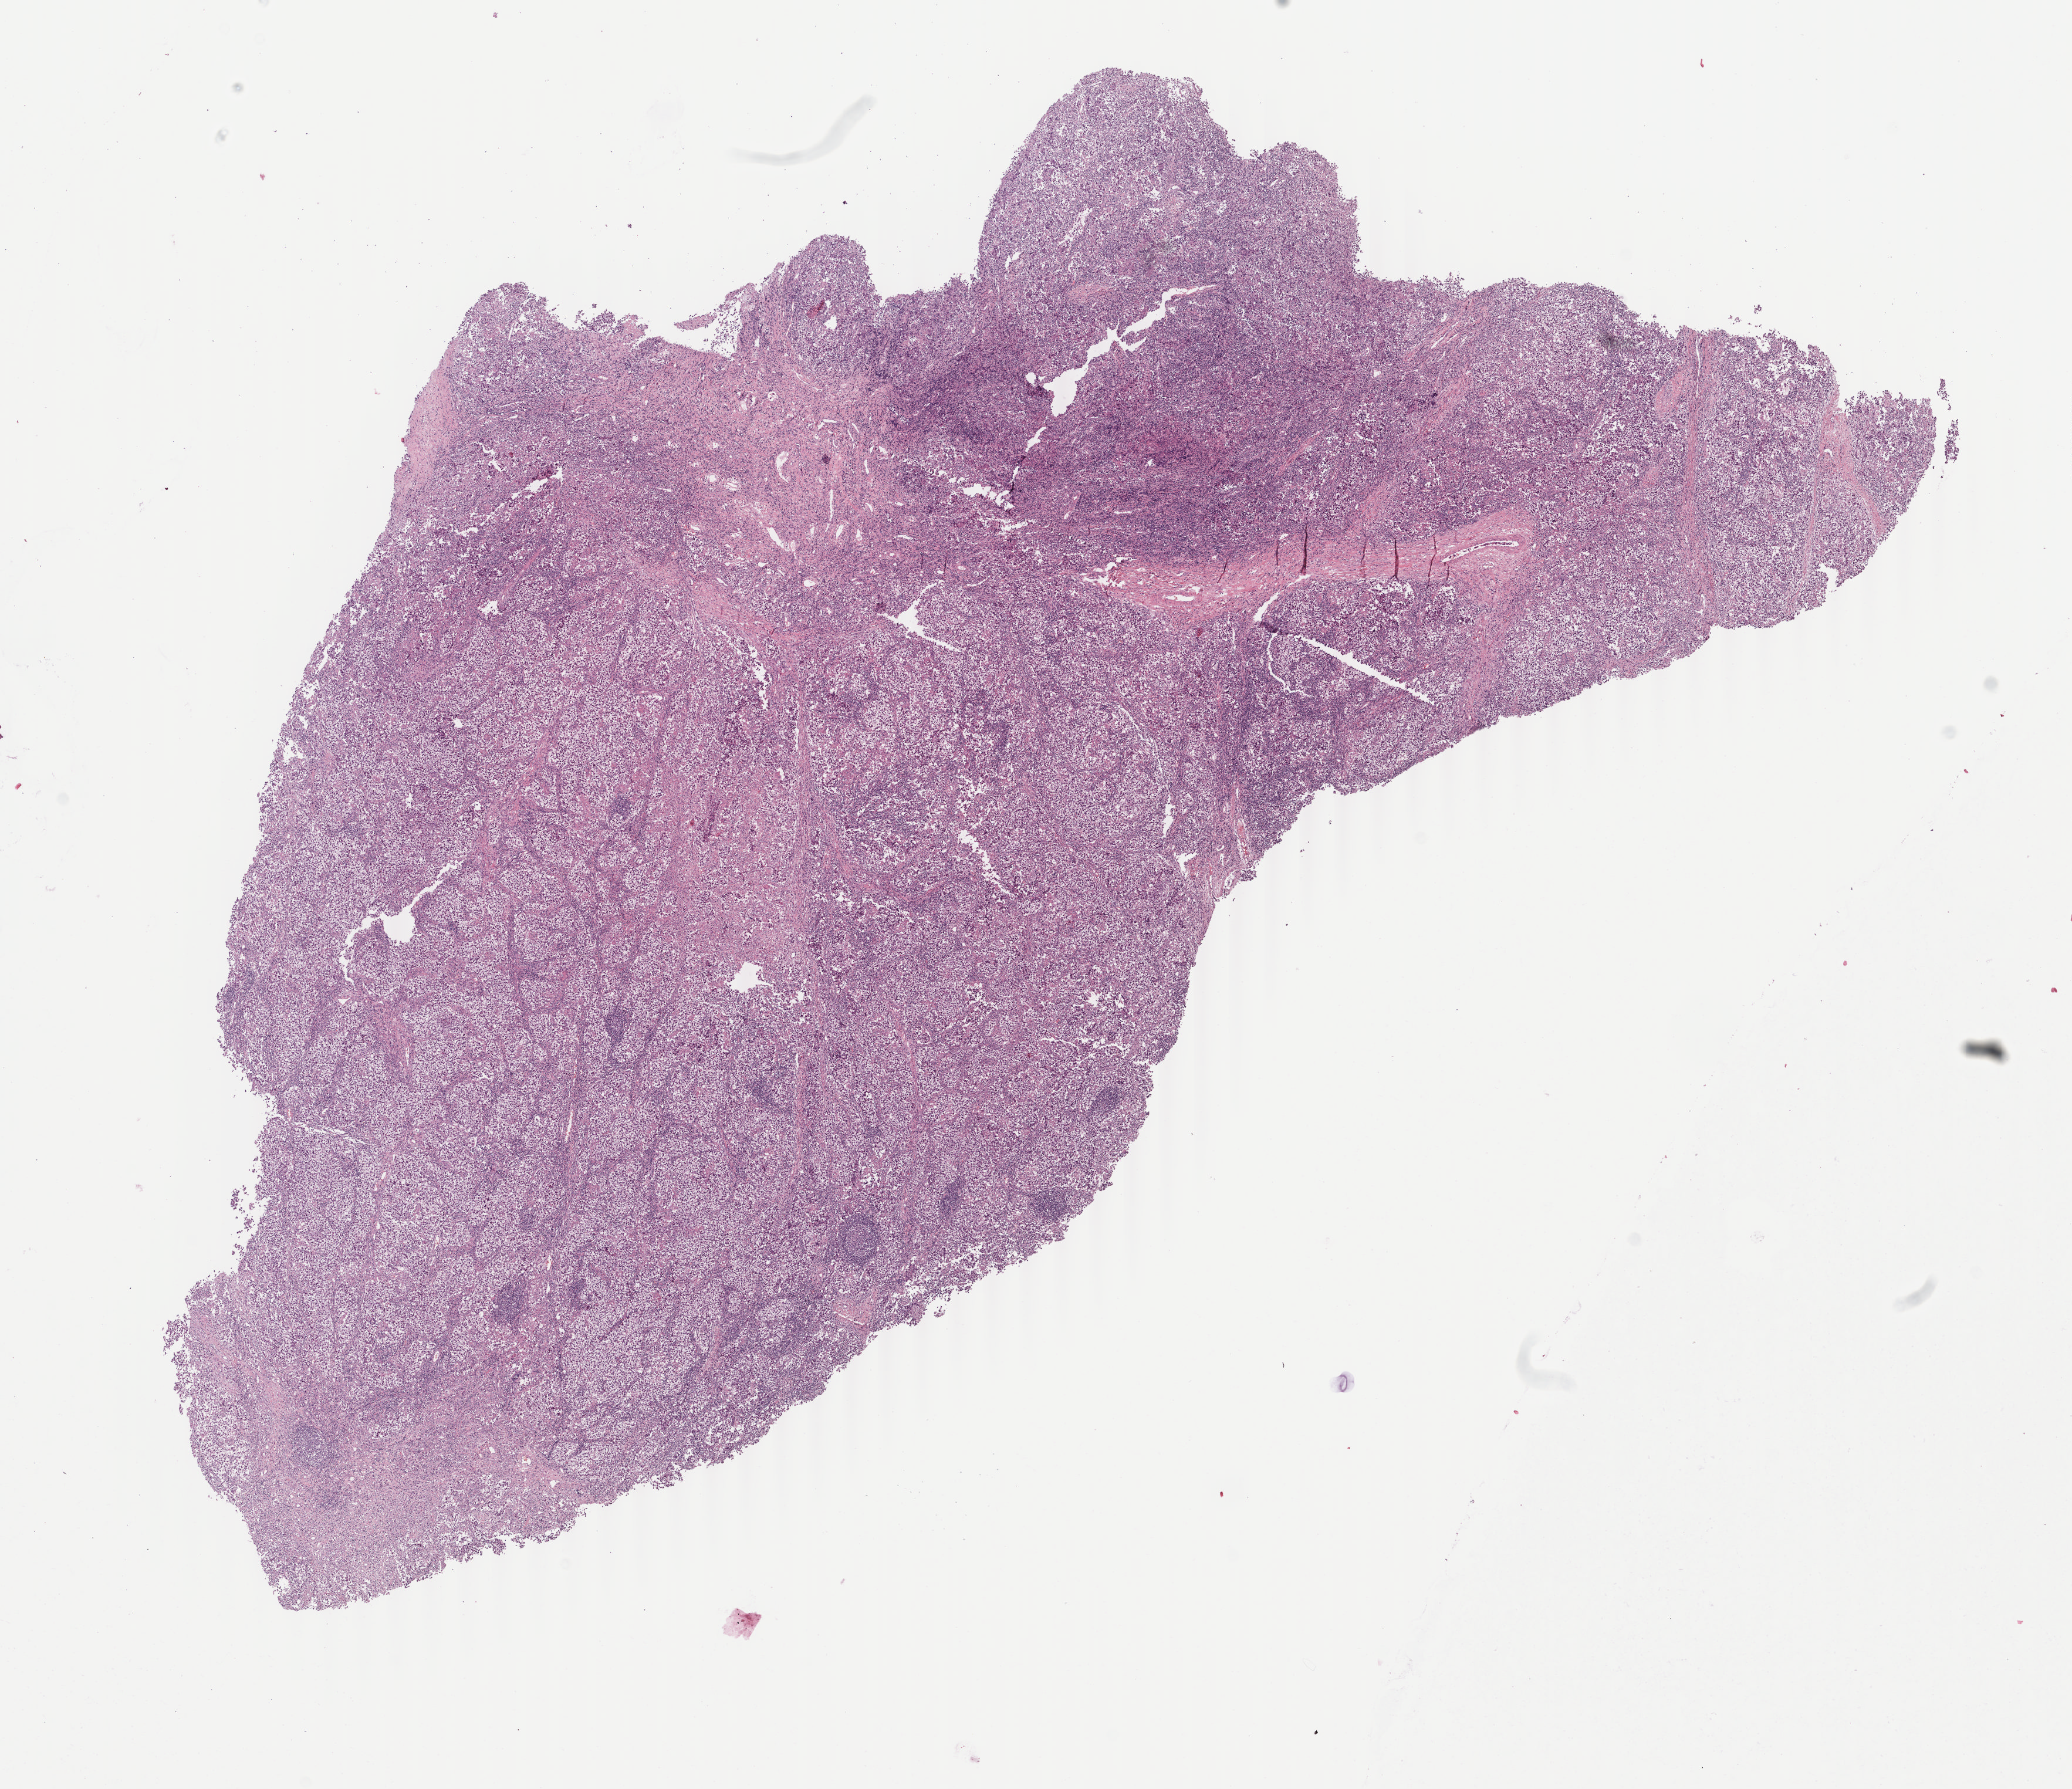
Digitized H&E tissue section (whole slide) — low-resolution overview of the scanned area, about 14.0 x 12.1 mm (from a 40x scan), FFPE section, primary tumour sample from the testis. Male, age 26 years at initial diagnosis.
Histologic diagnosis: Seminoma, NOS. TNM: T1 N0 M0. Laterality: left. AJCC pathologic stage: IA (7th edition).